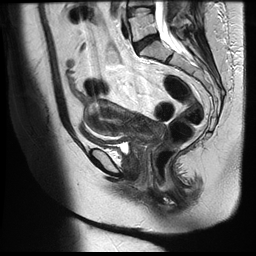
Pelvic MRI for cervical cancer, one sagittal slice. Slice 17 of 35 in the series (ordered by position). T2-weighted. 1.5 T. TE 122.8 ms, TR 4992 ms. 4 mm slice thickness. 256 × 256 image matrix, field of view 300 × 300 mm. Female patient, age 42 years.
Annotated regions visible in this slice (outlined manually by an expert reader):
- uterus and cervix: box from (x=83, y=99) to (x=165, y=160) px